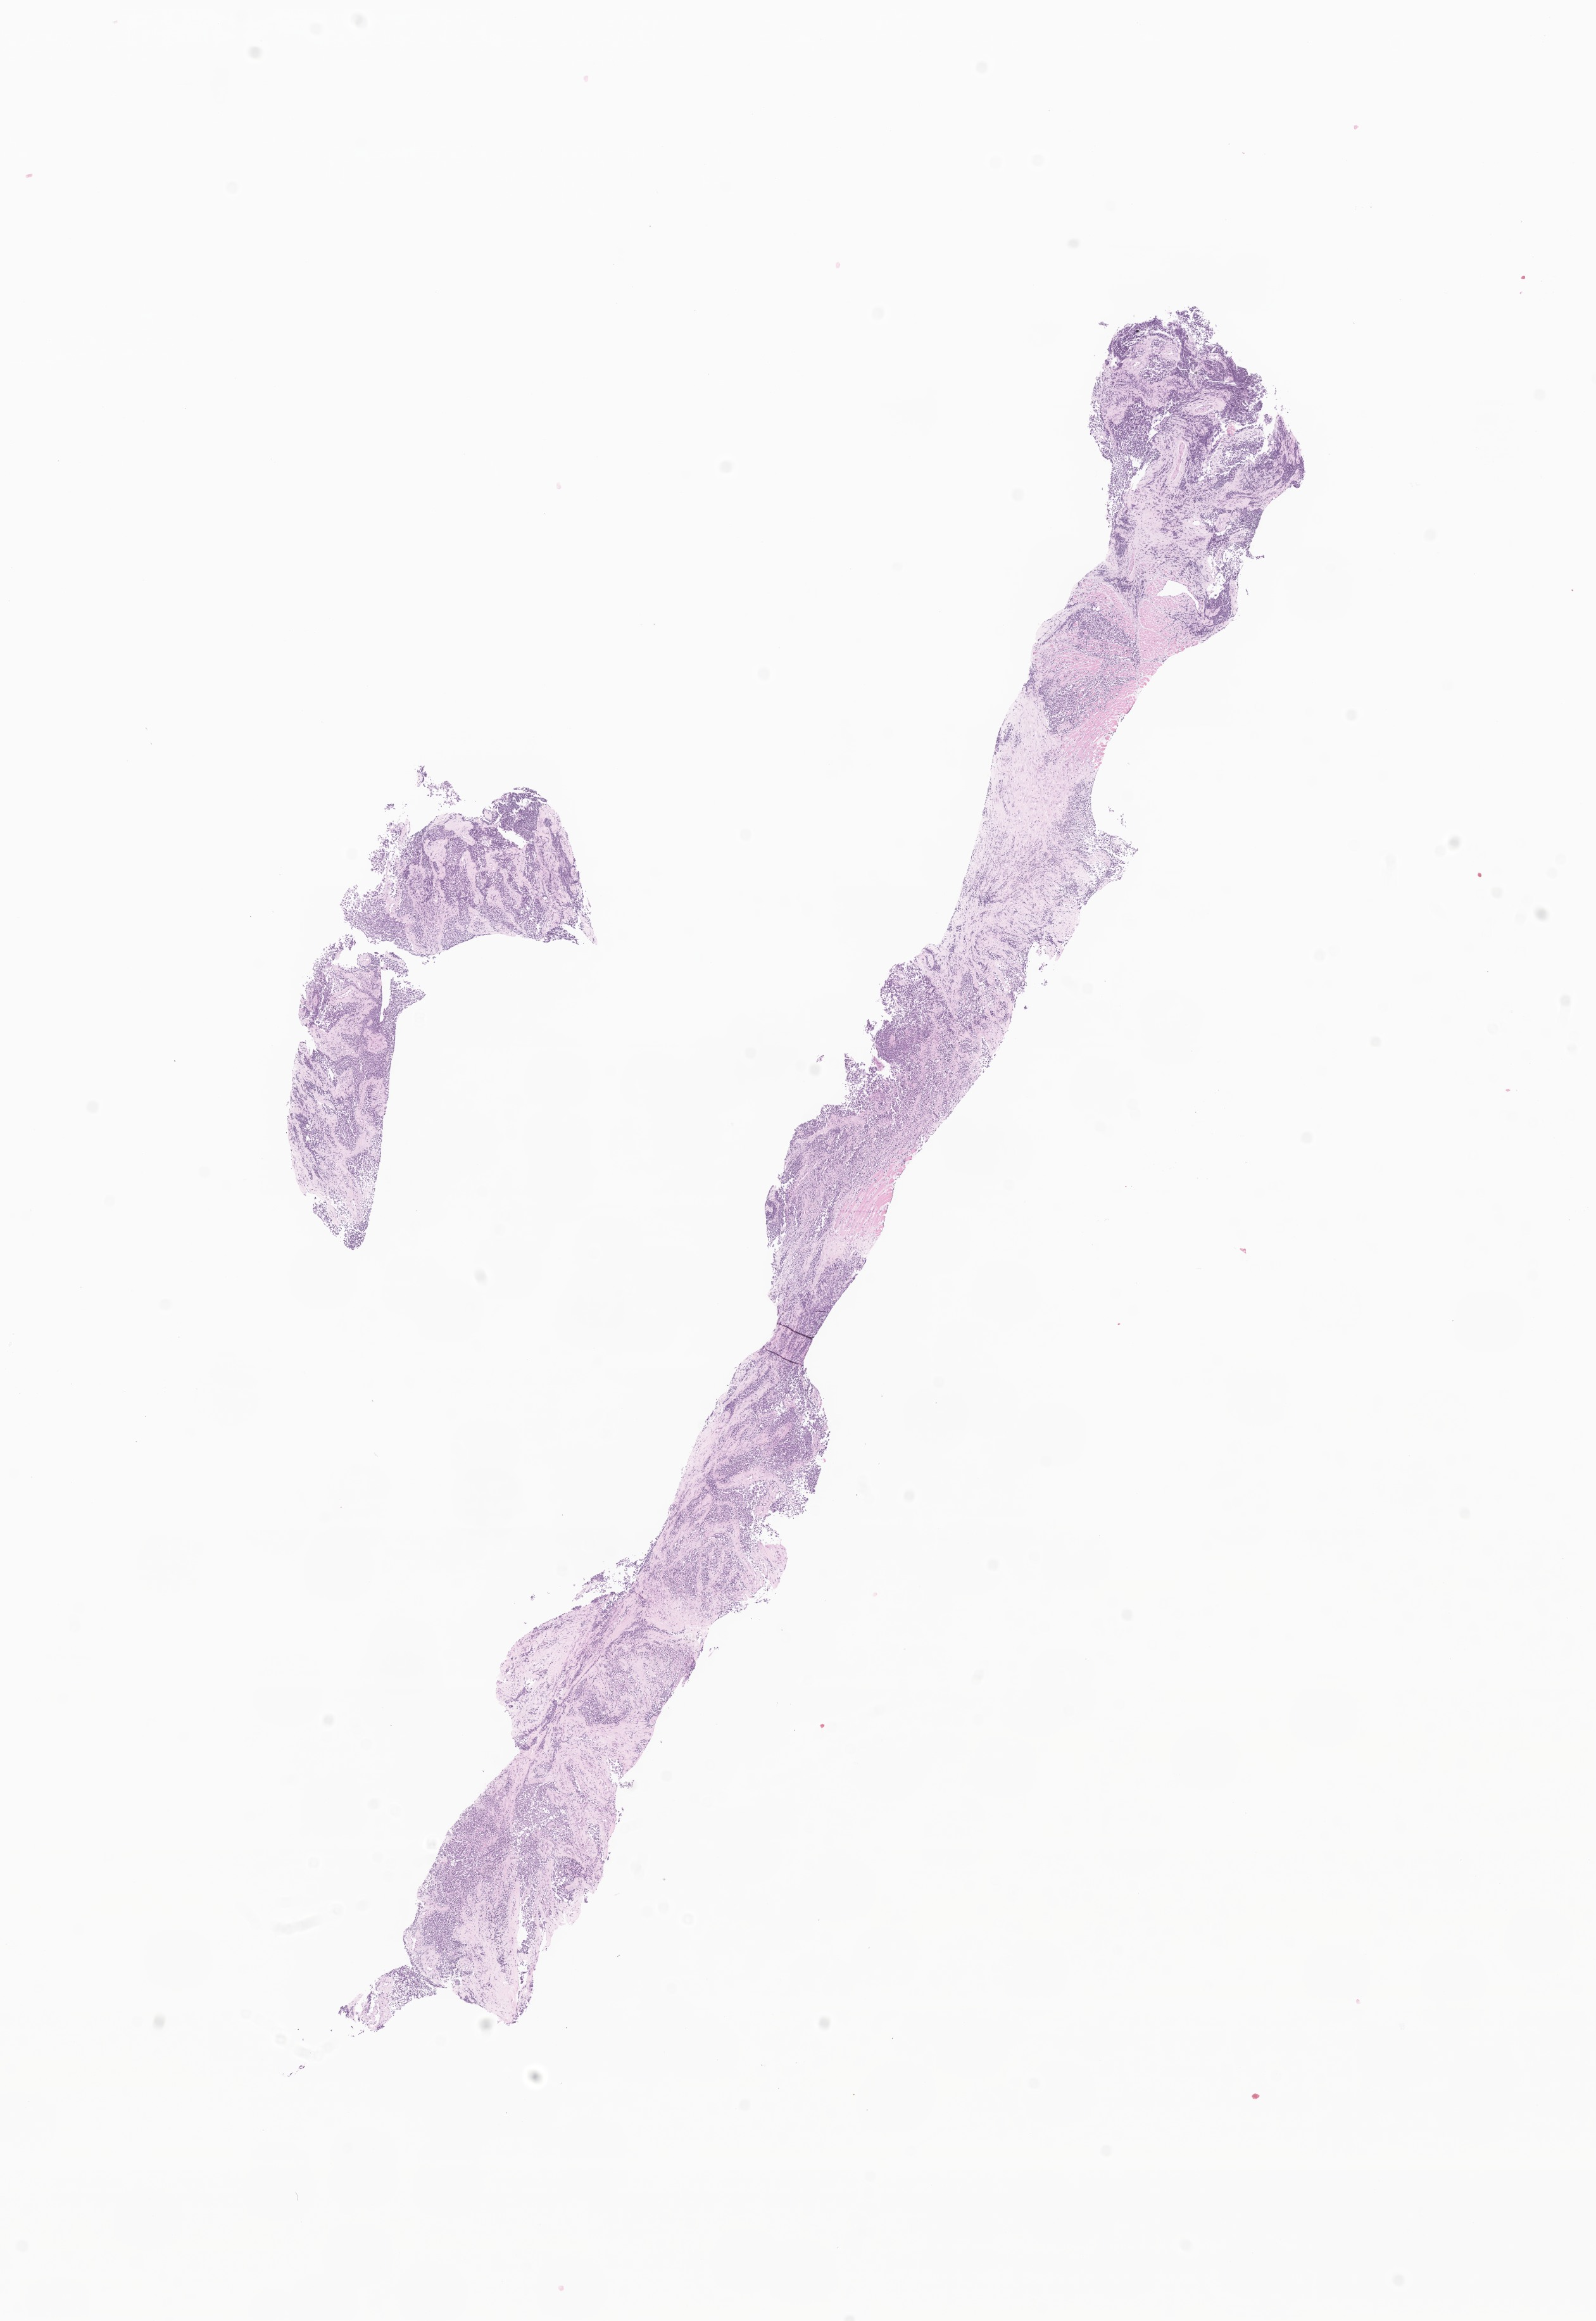
Whole-slide image, hematoxylin and eosin (H&E) stain of tumor tissue from the bronchus and lung, whole scanned area (about 10.6 x 15.5 mm) shown as a low-resolution overview. Formalin-fixed paraffin-embedded section. Female patient, age 107 days.
Tissue or organ of origin (case record): overlapping lesion of lung. Recorded diagnosis: Rhabdomyosarcoma, NOS.